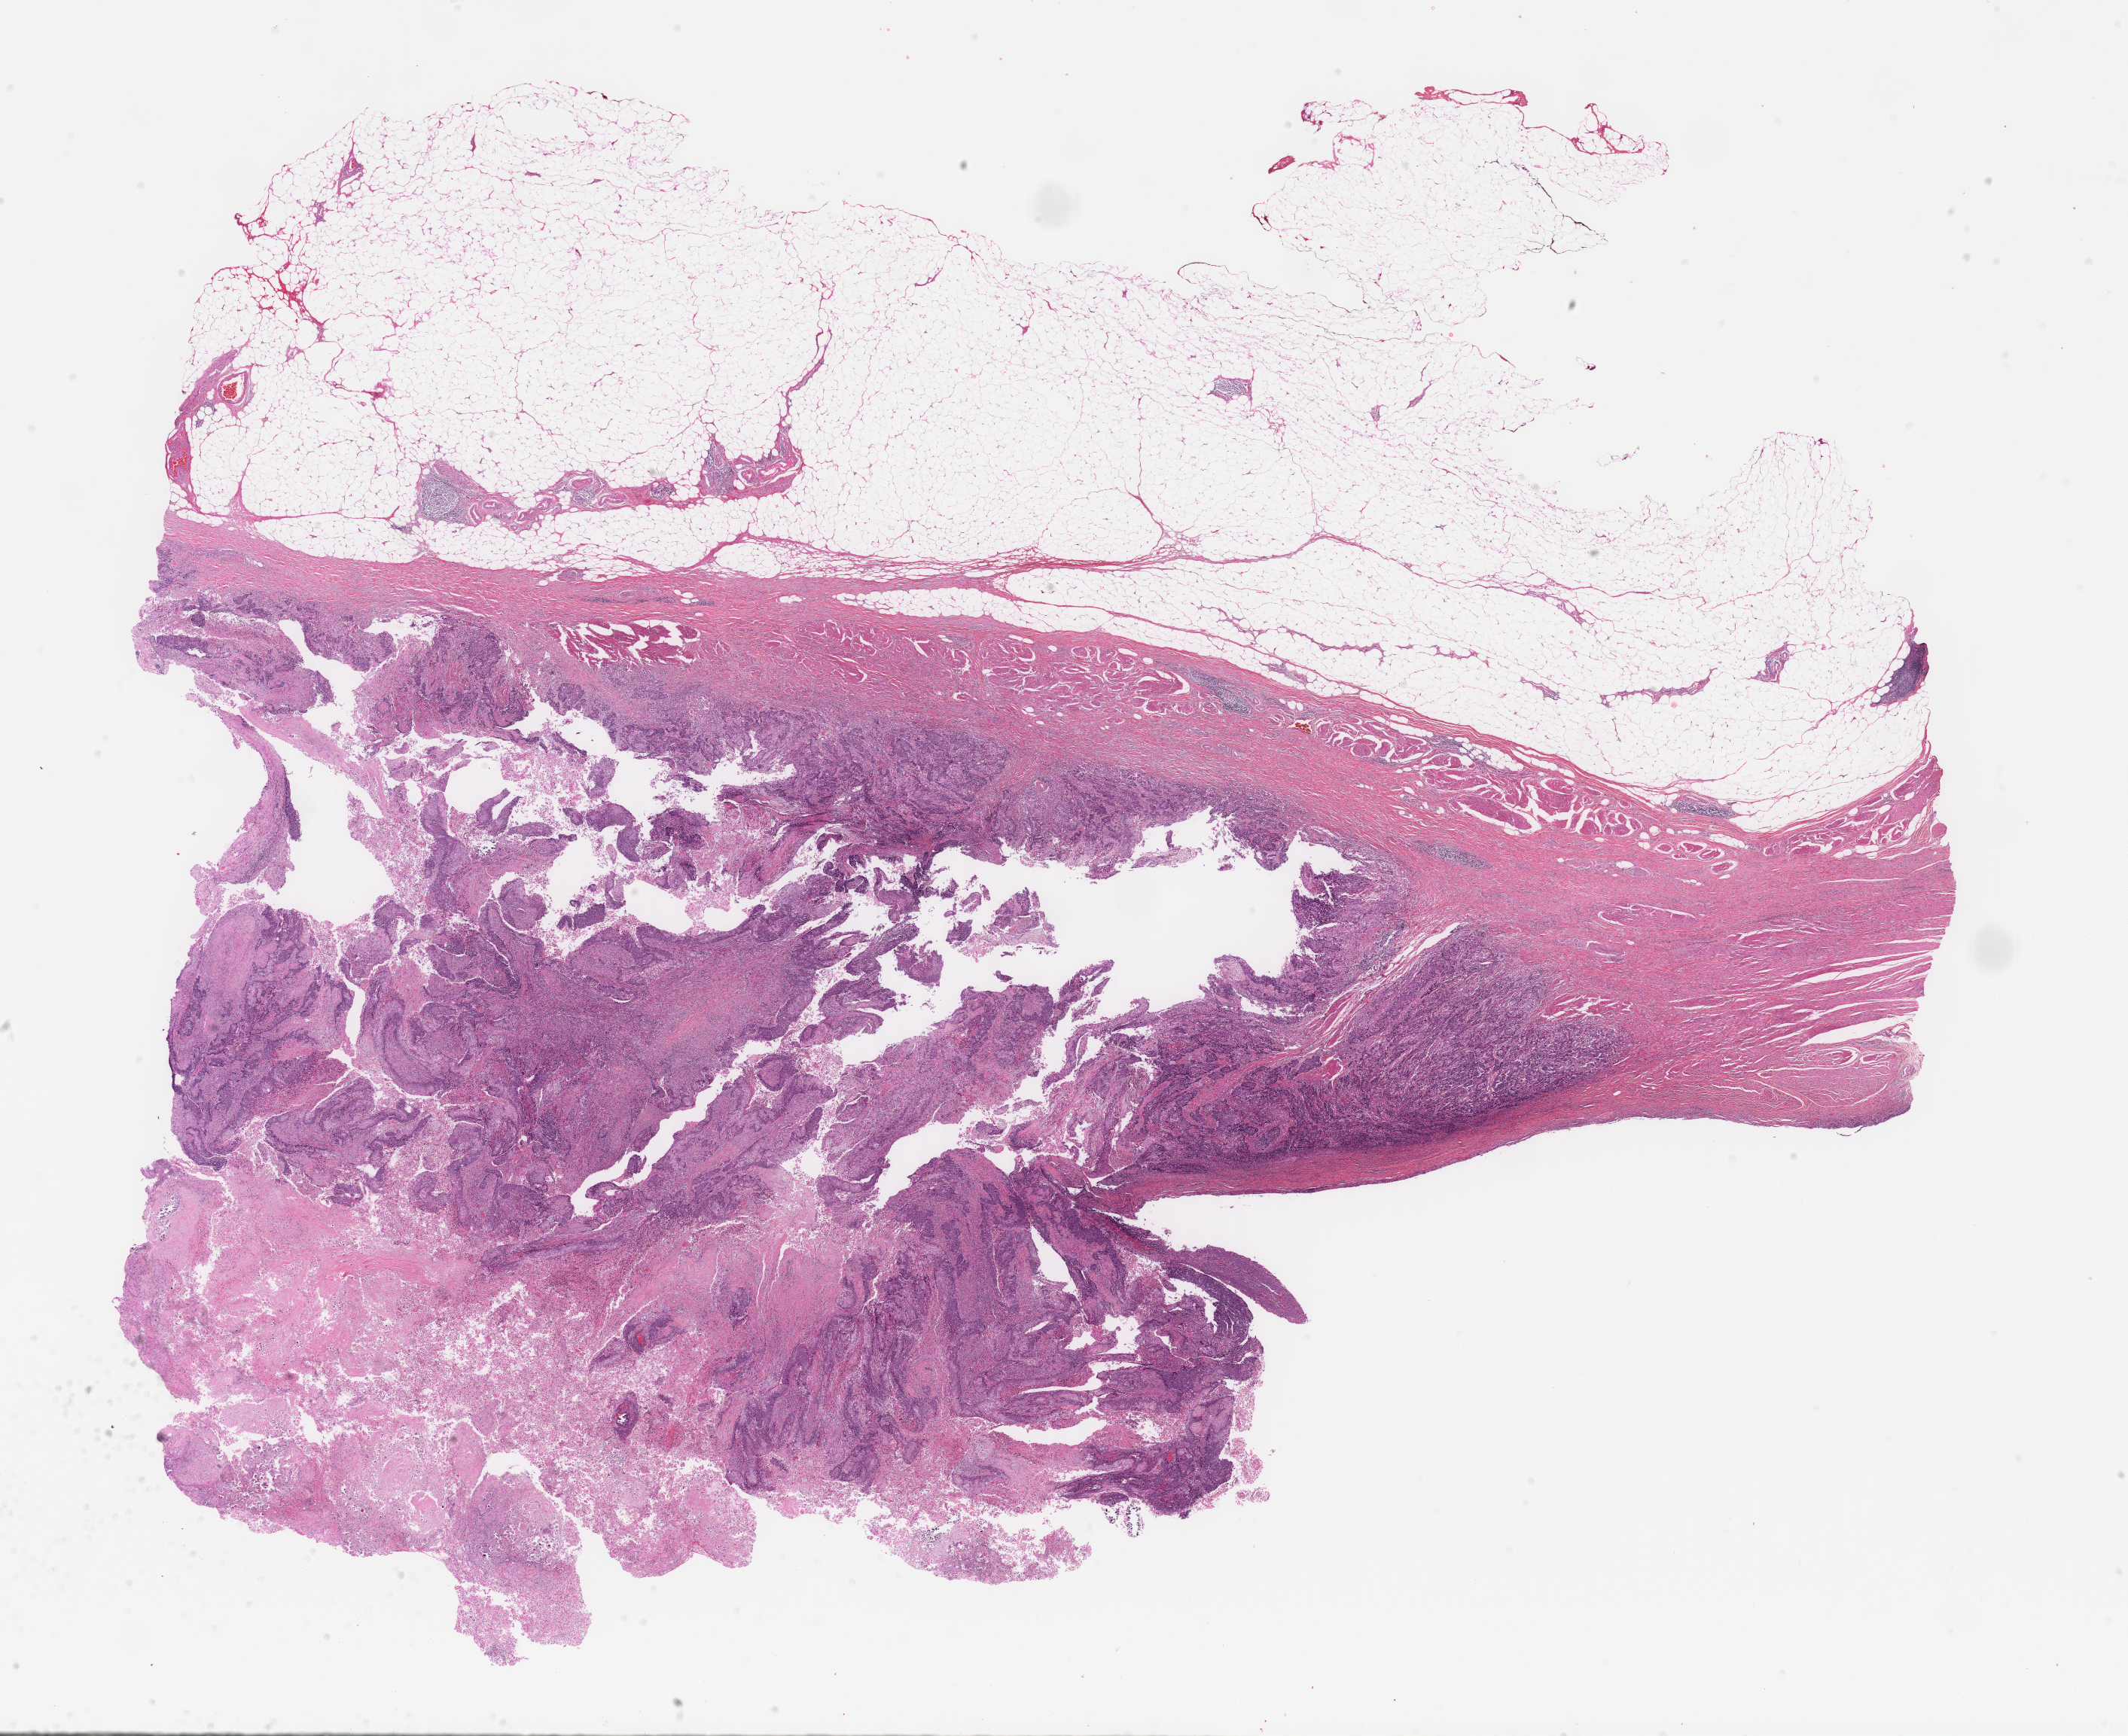
Digitized Hematoxylin and eosin (H&E) stained tissue section (whole slide) — shown as a low-resolution overview of the whole scanned area (about 22.4 x 18.3 mm), formalin-fixed paraffin-embedded (FFPE) diagnostic section, sample: primary tumour, bladder. Male, age 85 years at initial diagnosis. Histologic grade: high grade.
Histologic diagnosis: Transitional cell carcinoma. AJCC pathologic stage: II (6th edition). TNM: T3b N0 M0.